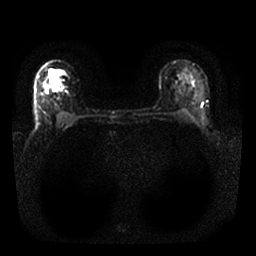
Breast MRI, one axial slice; slice 19 of 25 in the series (ordered by position); diffusion-weighted series; image 2 of 4 stored at this slice position (different b-values; order by instance number); 1.5 T; 256 × 256 image matrix. Female patient.
Outlined on this slice (manually delineated by an expert):
- tumour on diffusion-weighted imaging: box from (x=48, y=69) to (x=59, y=86) px